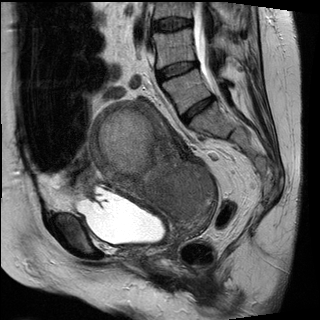
Pelvic MRI for cervical cancer, one sagittal slice. Position 16 of 30 along the scan axis. T2-weighted. 1.5 T. TE 89 ms, TR 2930 ms. 4 mm slice thickness. 320 × 320 image matrix, field of view 260 × 260 mm. Patient: female, 62 years.
Annotated regions visible in this slice (outlined manually by an expert reader):
- uterus and cervix: bounding box (x1, y1, x2, y2) in pixels: (91, 99, 214, 222)